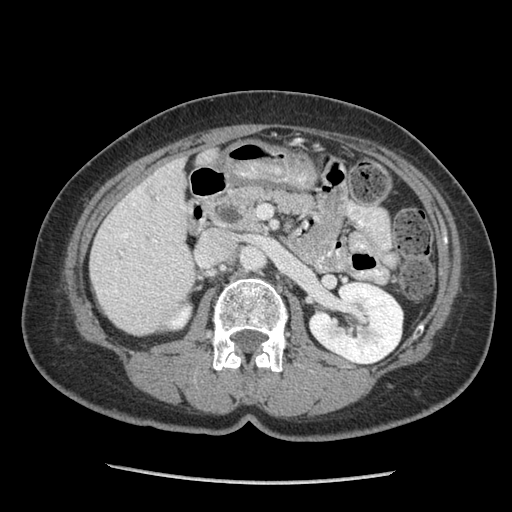
Contrast-enhanced abdominal CT (liver protocol), one axial slice; position 32 of 105 along the scan axis; 140 kVp; soft-tissue window (W 400 / L 40 HU); 2.5 mm slice thickness; 512 × 512 image matrix, field of view 340 × 340 mm. From the clinical record (not read from this slice): diagnosis: hepatocellular carcinoma (patient treated with transarterial chemoembolisation; whether this scan precedes or follows treatment is not stated here); TNM stage (as recorded): Stage-I; Child-Pugh class: A; tumour differentiation: moderately differentiated; tumour nodularity: uninodular.
Annotated regions visible in this slice (semi-automatic segmentation, software-assisted and operator-edited):
- liver parenchyma outside the tumour (the mass and vessels are separate outlines, so this box may not span the whole liver): bounding box (x1, y1, x2, y2) in pixels: (90, 148, 218, 334)
- liver vessels: (105, 187, 184, 302)